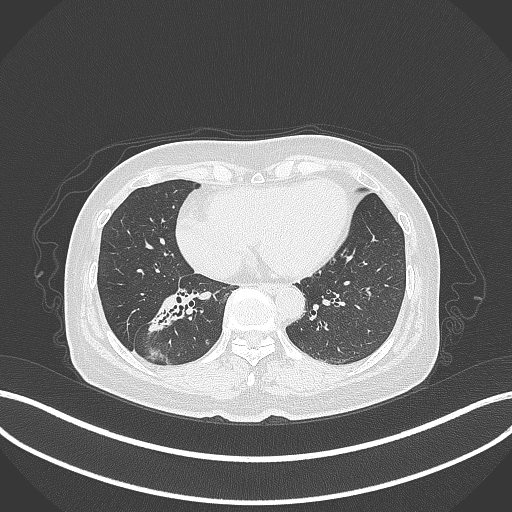
Chest CT, one axial slice; slice 142 of 429 in the series (ordered by position); reconstruction kernel B70f; 120 kVp; lung window (W 1500 / L -600 HU); 1 mm slice thickness; 512 × 512 image matrix, field of view 400 × 400 mm. Female patient, age 67 years. From the clinical record (not read from this slice): clinical TNM (as recorded): T1c N1 M0; histopathological grade: G2-3.
Structures marked on this image (rectangle marked by the reading radiologist):
- lung tumour (recorded histology: adenocarcinoma): bounding box <144,288,196,337> (left, top, right, bottom; pixels)